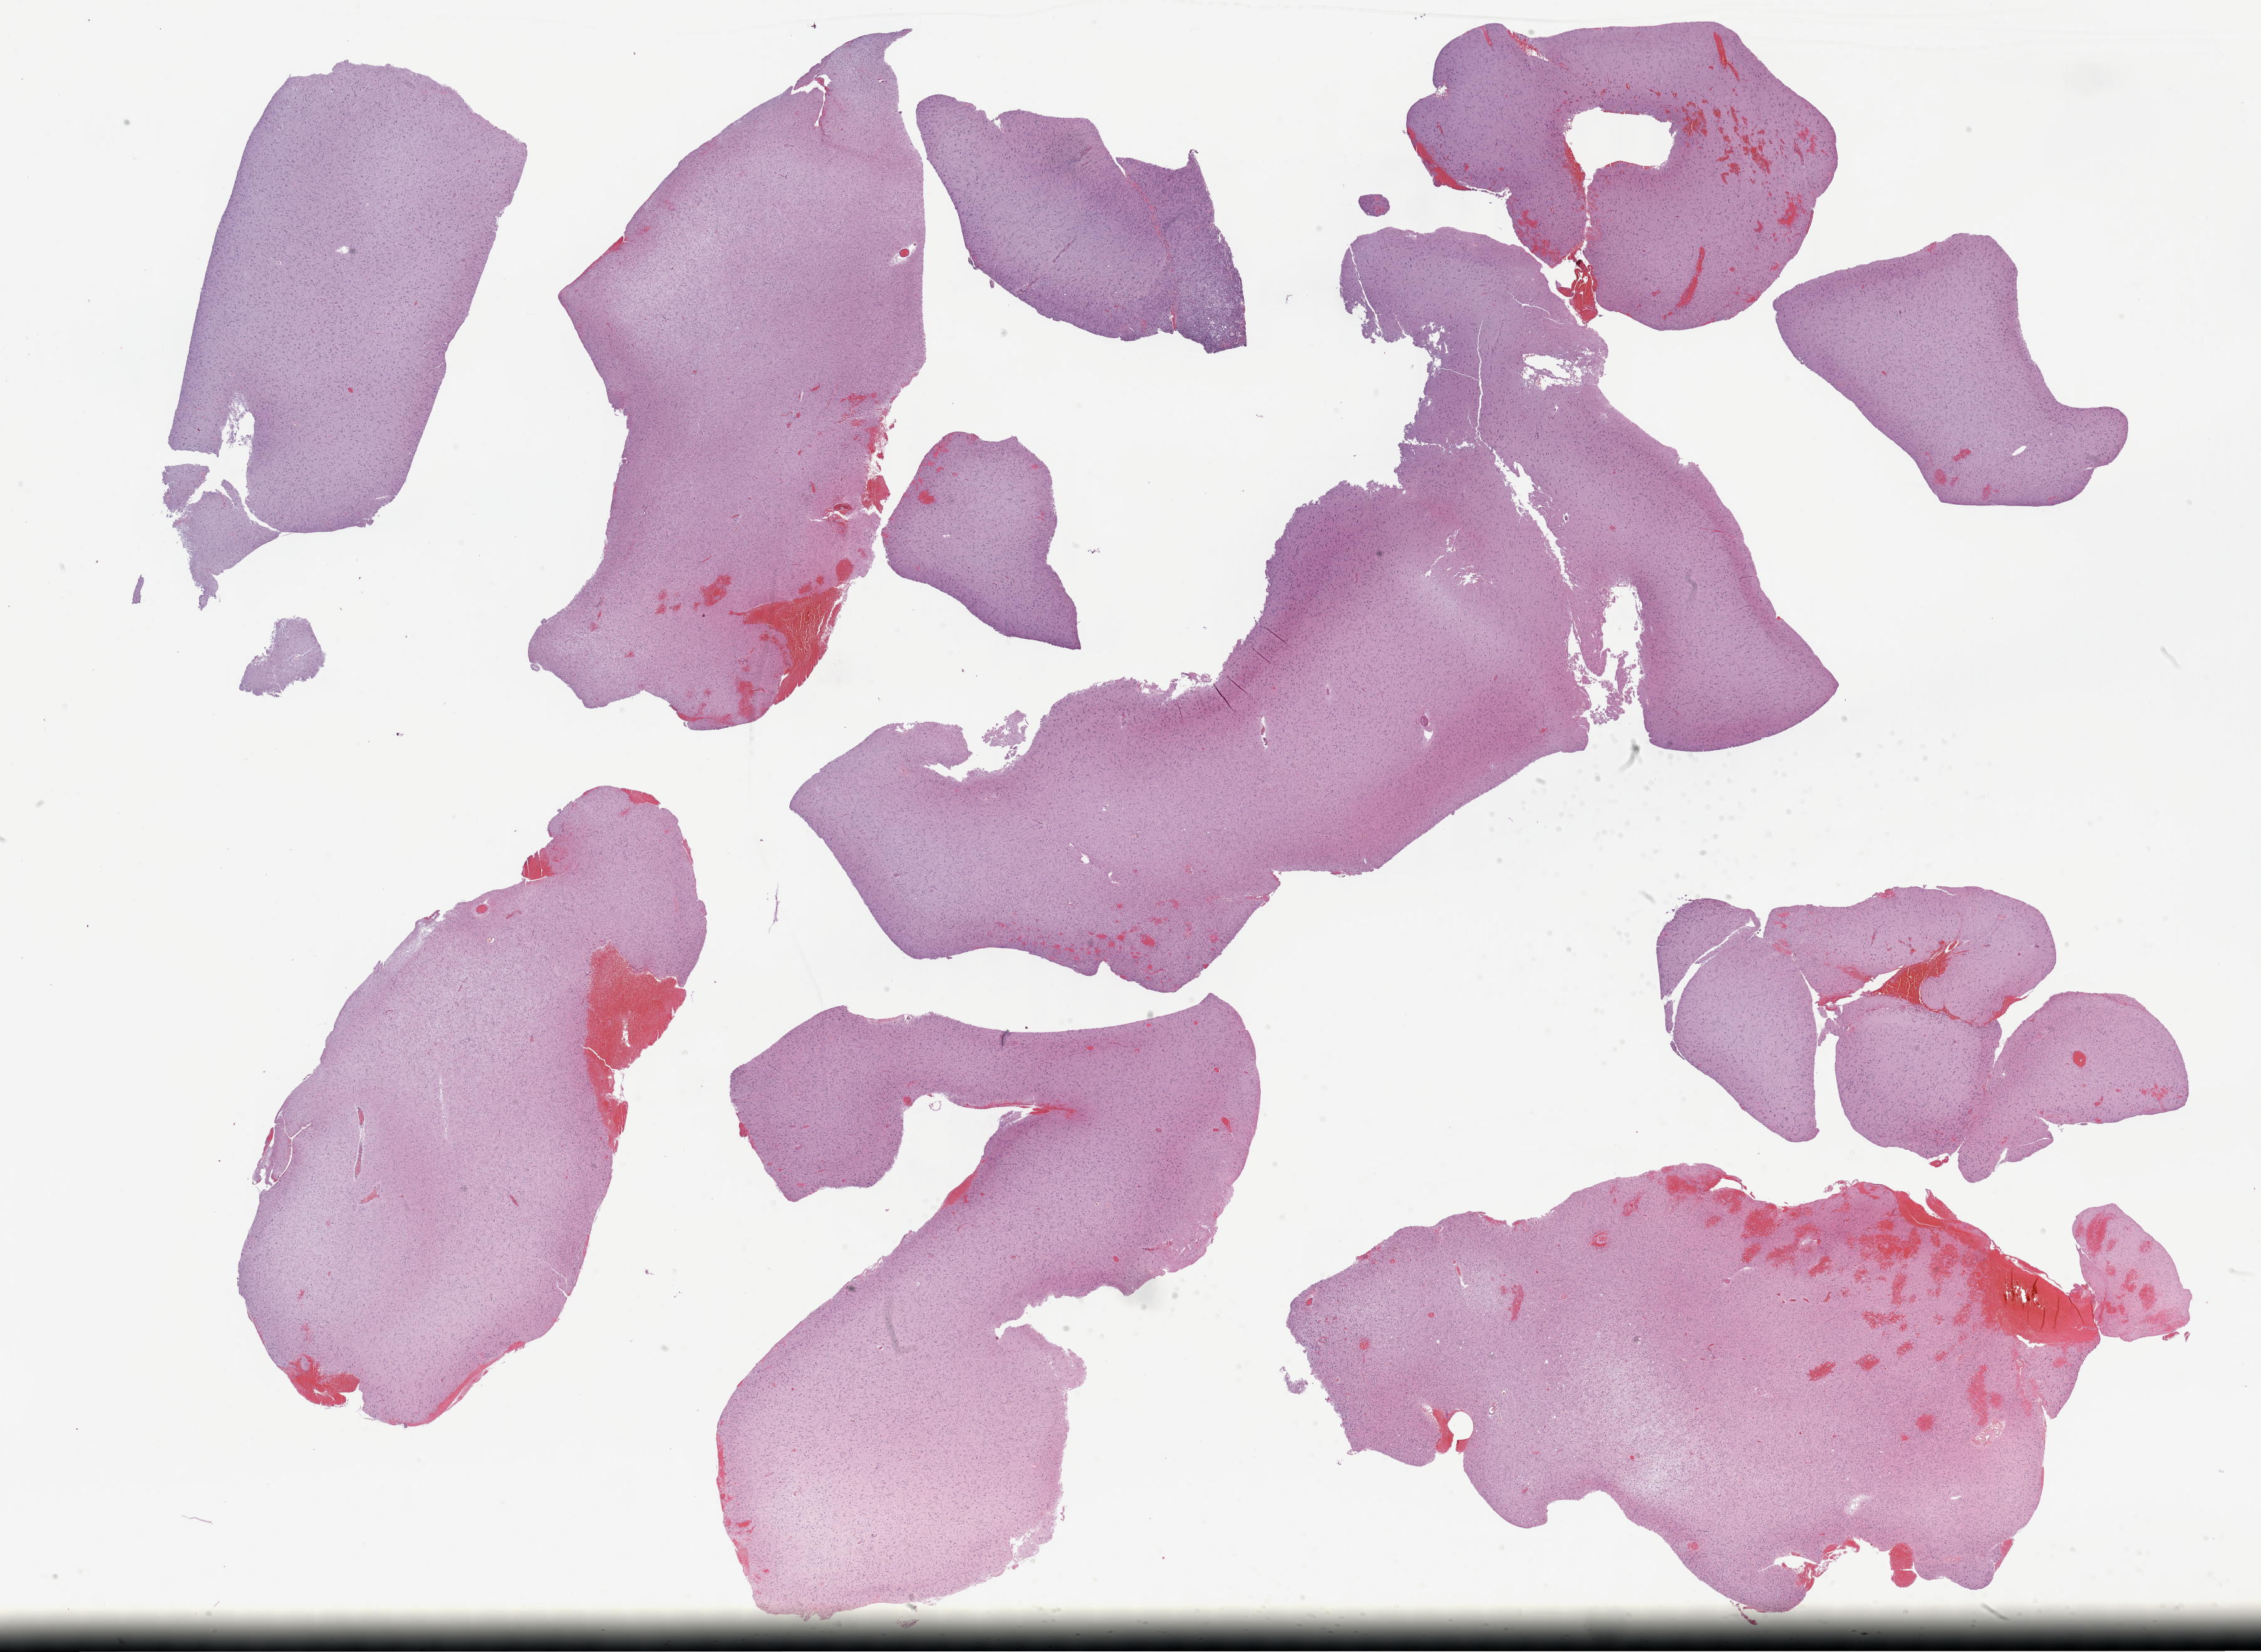
Whole-slide histology image, H&E, shown as a low-resolution overview of the whole scanned area (about 29.2 x 21.3 mm); formalin-fixed paraffin-embedded (FFPE) diagnostic section; sample: primary tumour, brain. Patient: male, age at initial diagnosis 54 years. Histologic grade: G2 (moderately differentiated).
Histologic diagnosis: Oligodendroglioma, NOS (cerebrum).